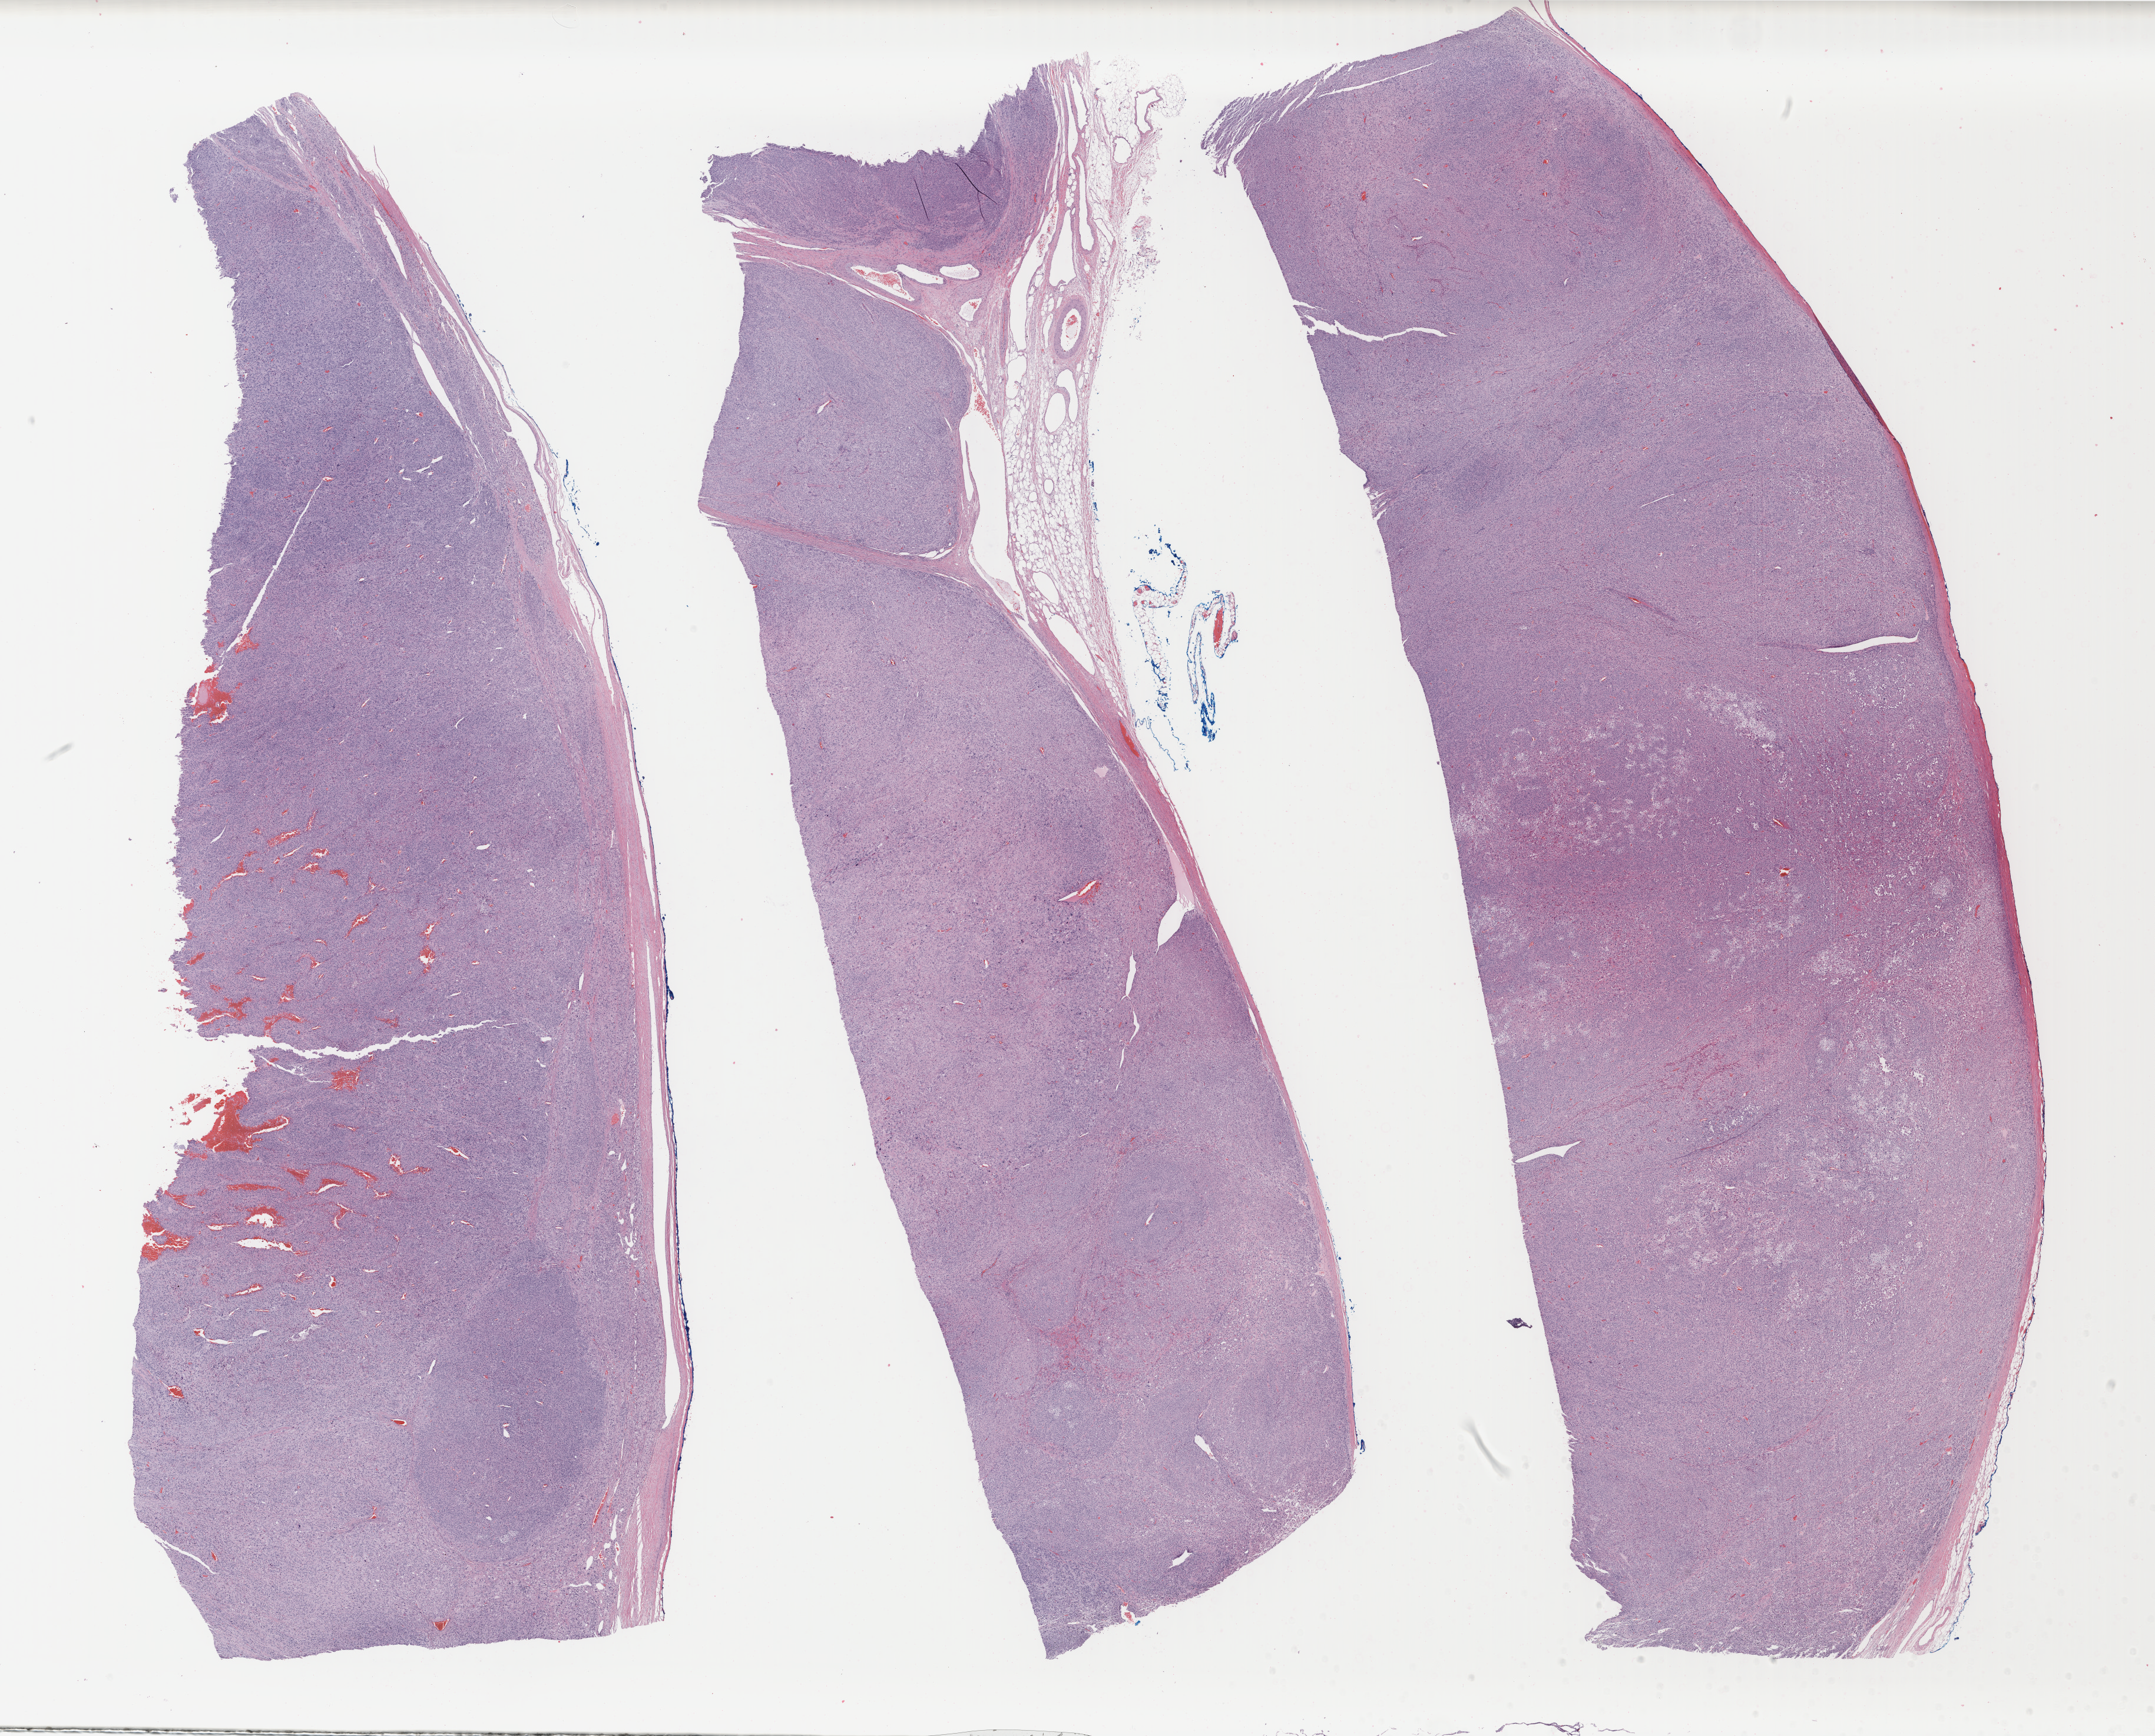
Whole-slide histology image, H&E-stained, shown as a low-resolution overview of the whole scanned area (about 29.0 x 23.4 mm, from a 40x scan); FFPE section; primary tumour sample from the adrenal cortex. Patient: female, age at initial diagnosis 53 years.
Laterality: left. Histologic diagnosis: Adrenal cortical carcinoma (cortex of adrenal gland).